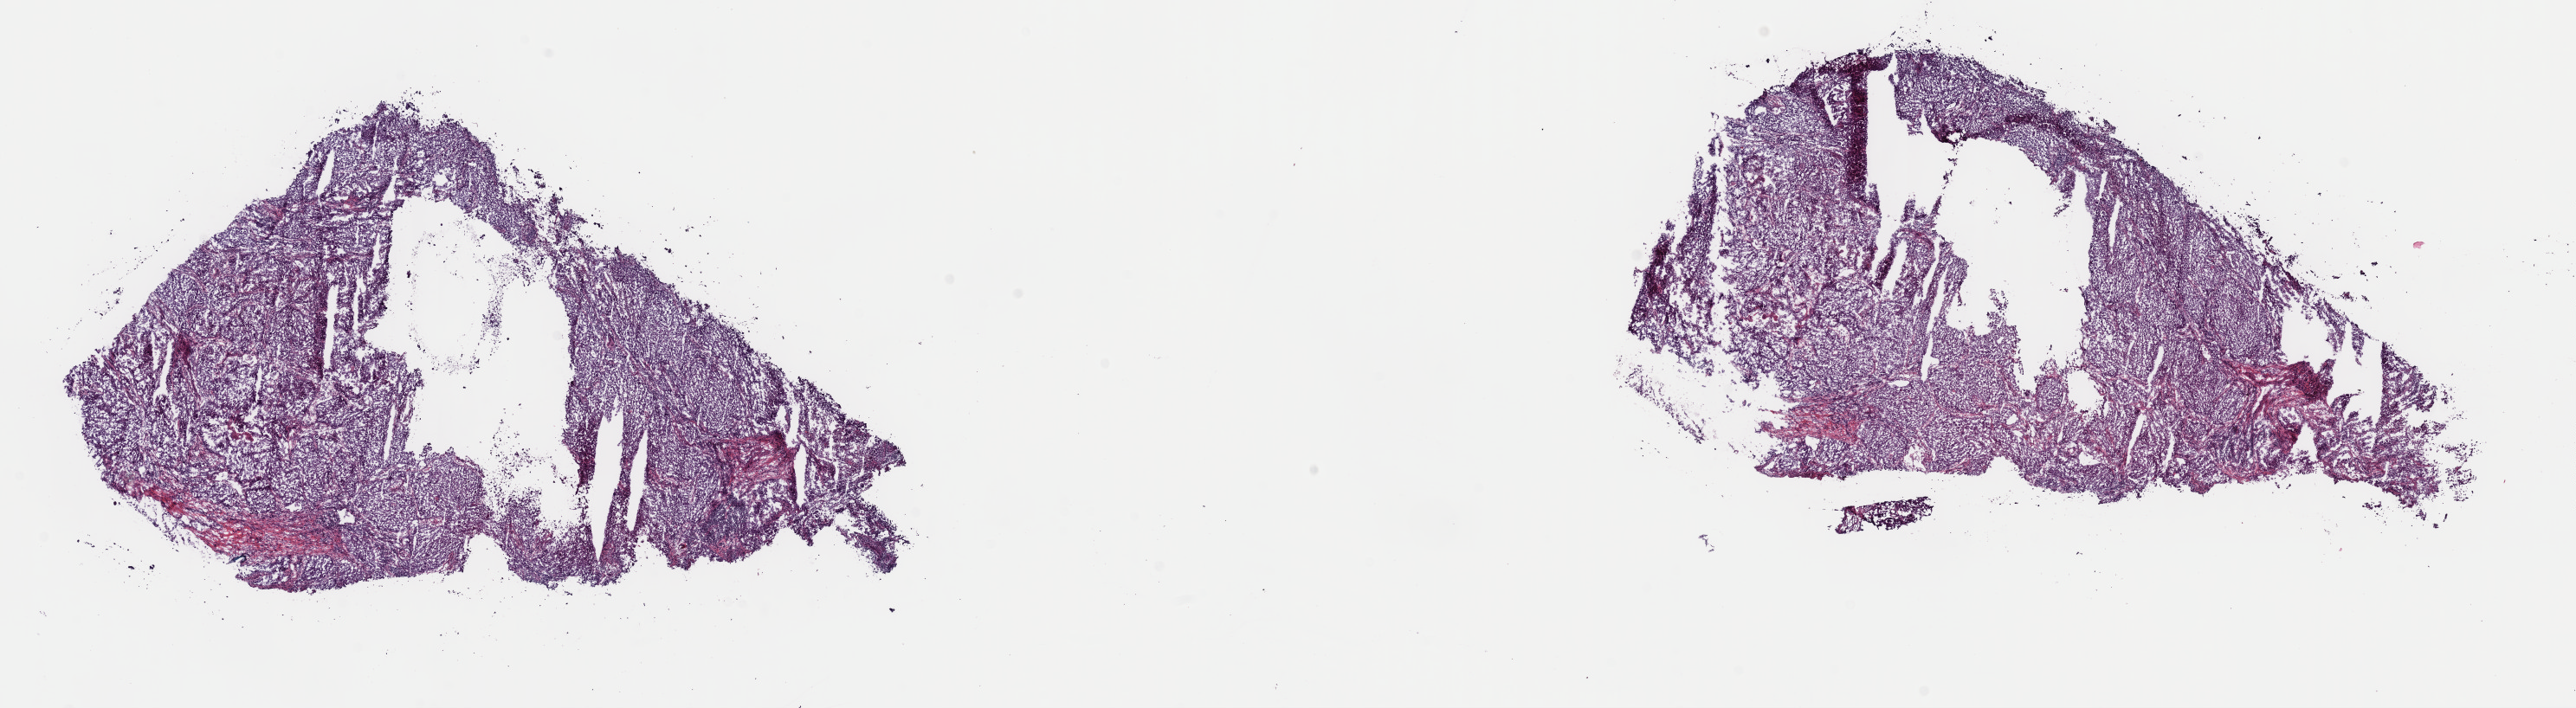
H&E-stained whole-slide image — a low-resolution overview of the entire scanned area, about 23.5 x 6.5 mm (from a 40x scan); frozen section; sample: primary tumour, lung. Male patient; age at initial diagnosis 57 years. Composition of this section per pathologist review: tumour cells 90%, tumour nuclei 95%, normal cells 0%, stromal cells 10%, necrosis 0%. Inflammatory infiltration, as recorded: lymphocyte infiltration 6%, monocyte infiltration 3%, neutrophil infiltration 10%.
- diagnosis: Squamous cell carcinoma, NOS (upper lobe, lung)
- AJCC pathologic stage: IIA